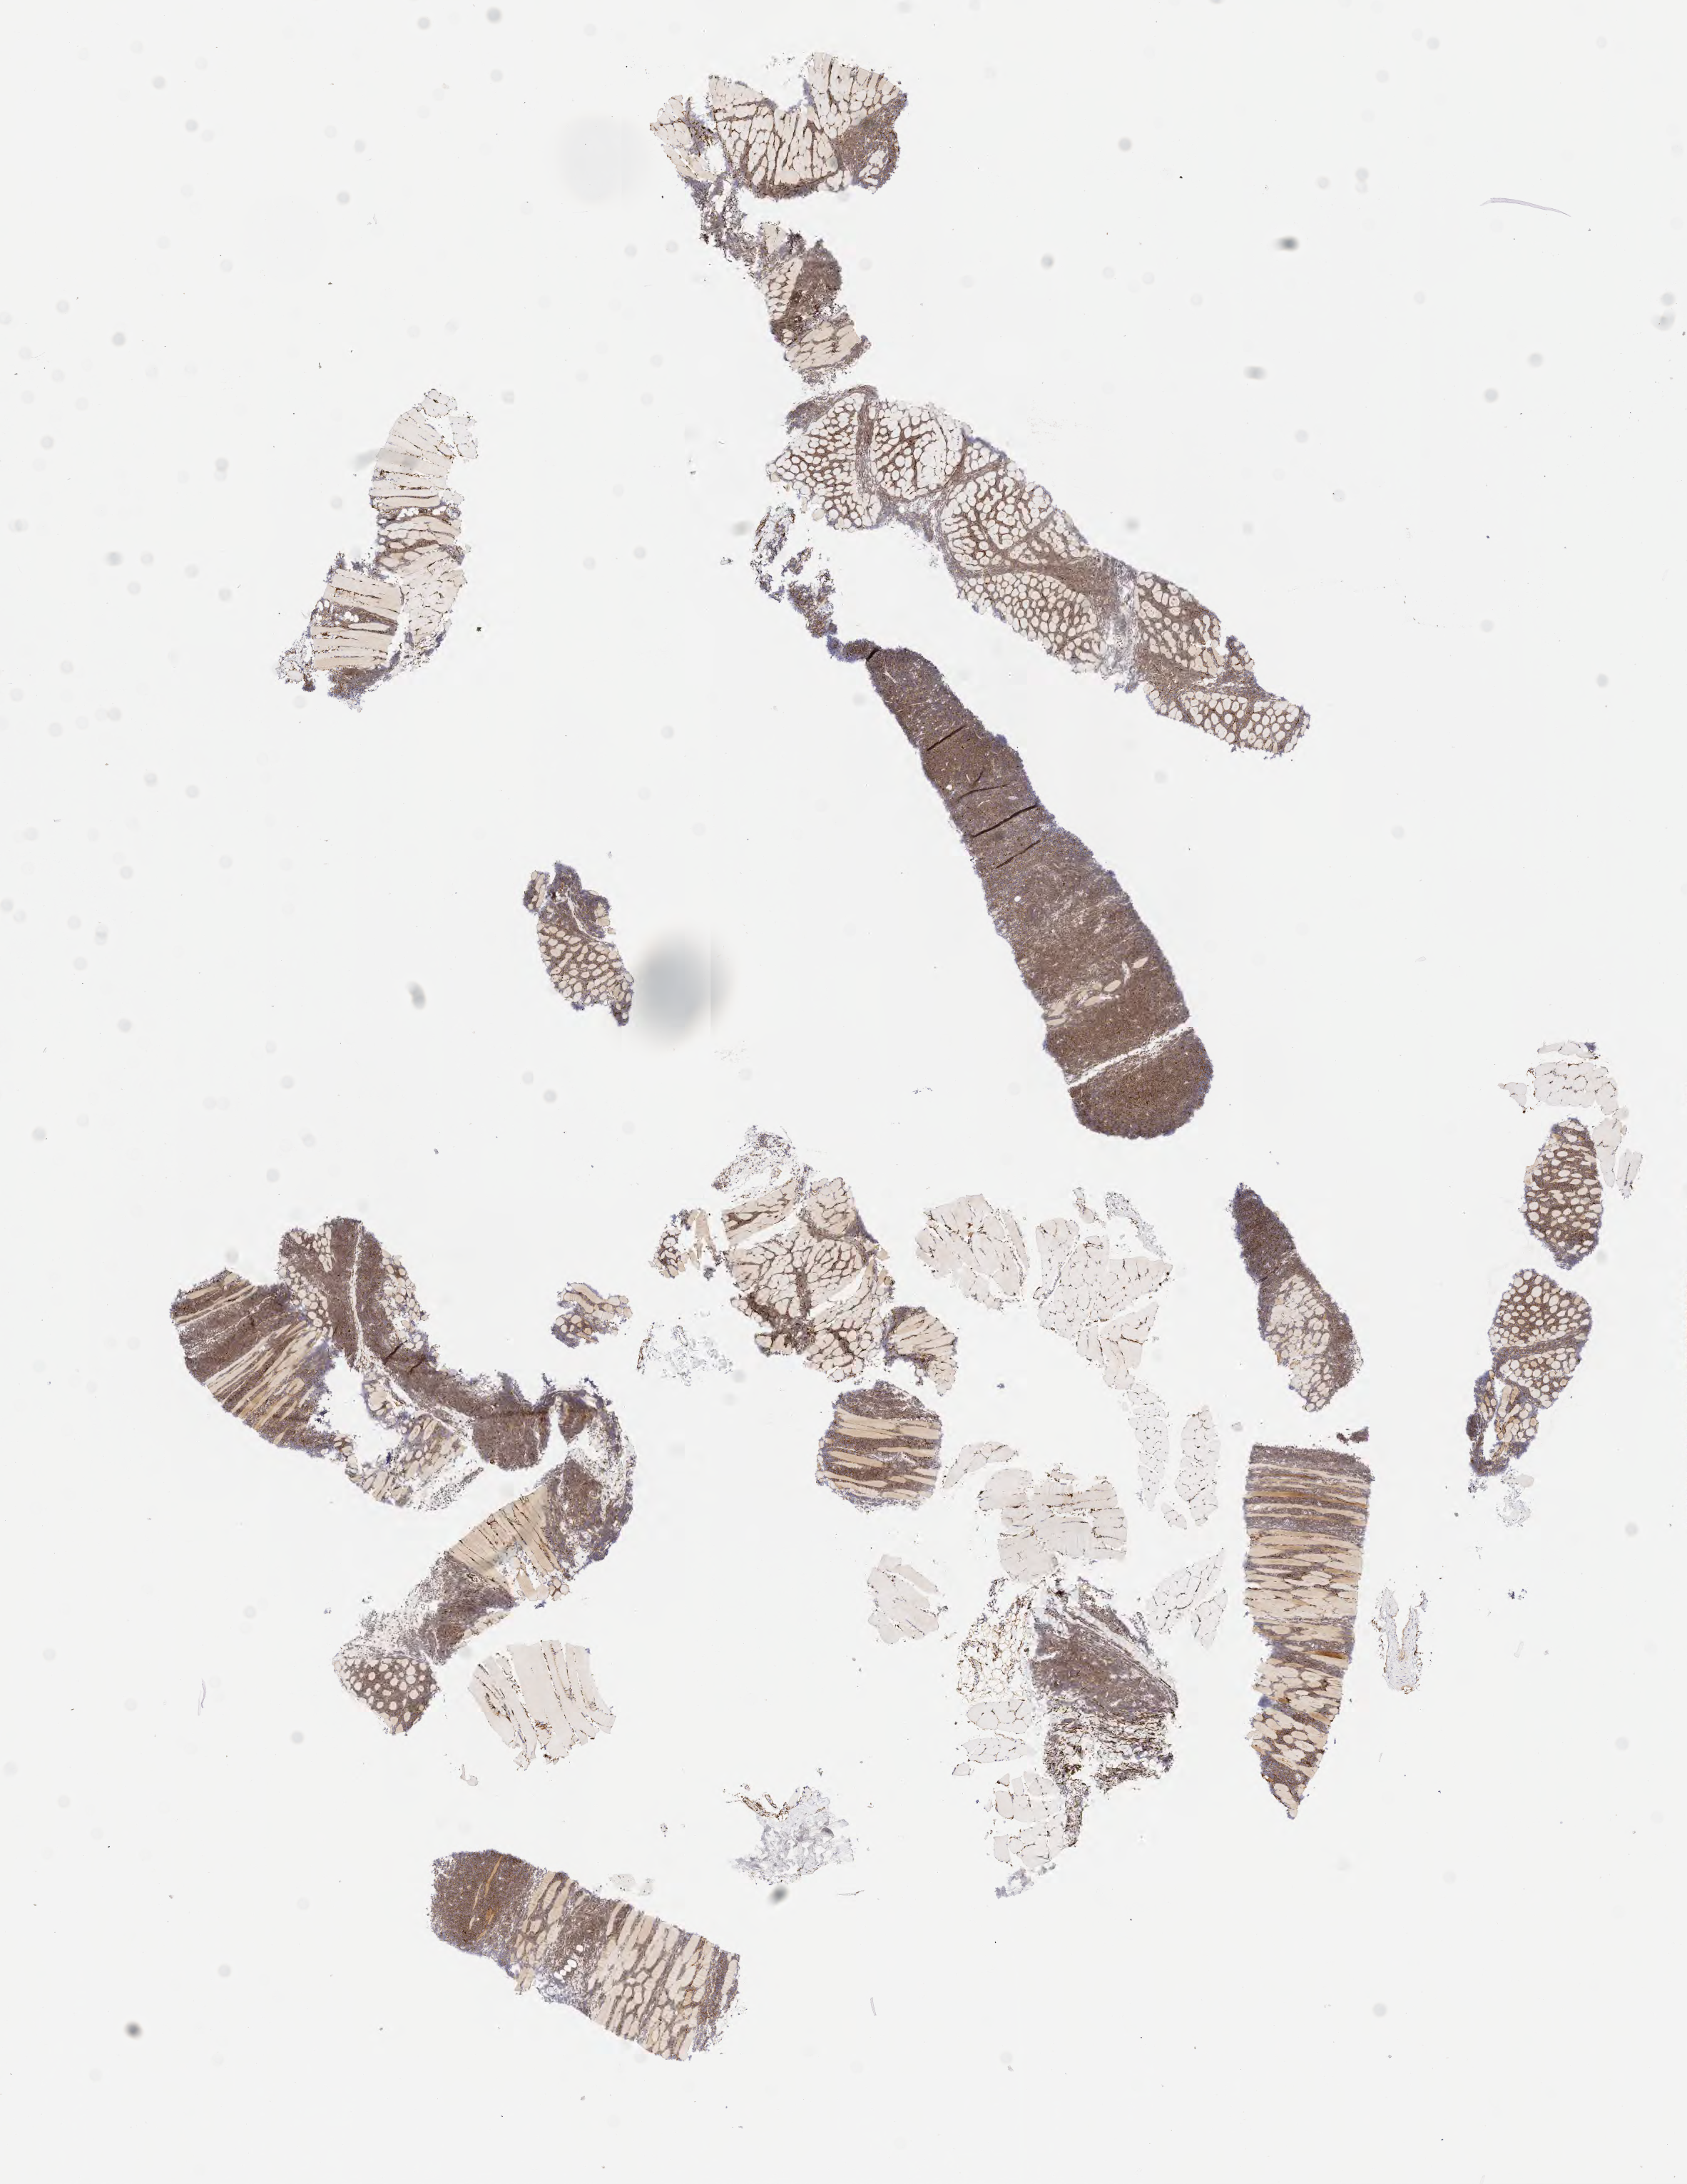
Whole-slide image, immunohistochemical stain for CD10, whole scanned area (about 9.6 x 12.4 mm) shown as a low-resolution overview; specimen: tumor tissue; anatomic site: retroperitoneum. Female patient, age 53 years.
Diagnosis: Burkitt lymphoma, NOS.